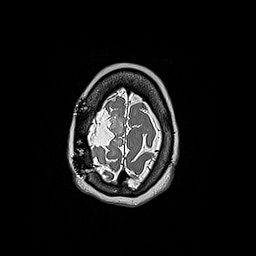
Brain MRI from a brain-tumour surgery series, one axial slice; slice 42 of 192 in the series (ordered by position); 1 mm slice thickness; 256 × 256 image matrix, field of view 250 × 250 mm. From the clinical record (not read from this slice): histopathology: Oligodendroglioma; WHO grade: 3; IDH mutation: yes.
Structures marked on this image (manually delineated by an expert):
- tumour: bounding box <89,138,95,148> (left, top, right, bottom; pixels)